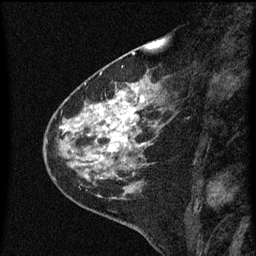
Breast MRI (dynamic contrast-enhanced), one sagittal slice. Position 20 of 60 along the scan axis. Dynamic contrast-enhanced series, image 2 of 3 at this slice position (ordered by acquisition). 1.5 T. TE 4.2 ms, TR 8 ms. 256 × 256 image matrix, field of view 180 × 180 mm. Patient: female, 60 years.
Annotated regions visible in this slice (semi-automatically segmented with operator editing):
- analysis volume of interest (the breast-tissue region the enhancement analysis was run in; not a lesion): bounding box [x1, y1, x2, y2] px = [48, 82, 159, 183]
- tumour enhancement mask (voxels above the 70 % enhancement threshold inside the analysis volume of interest): [64, 88, 145, 161]